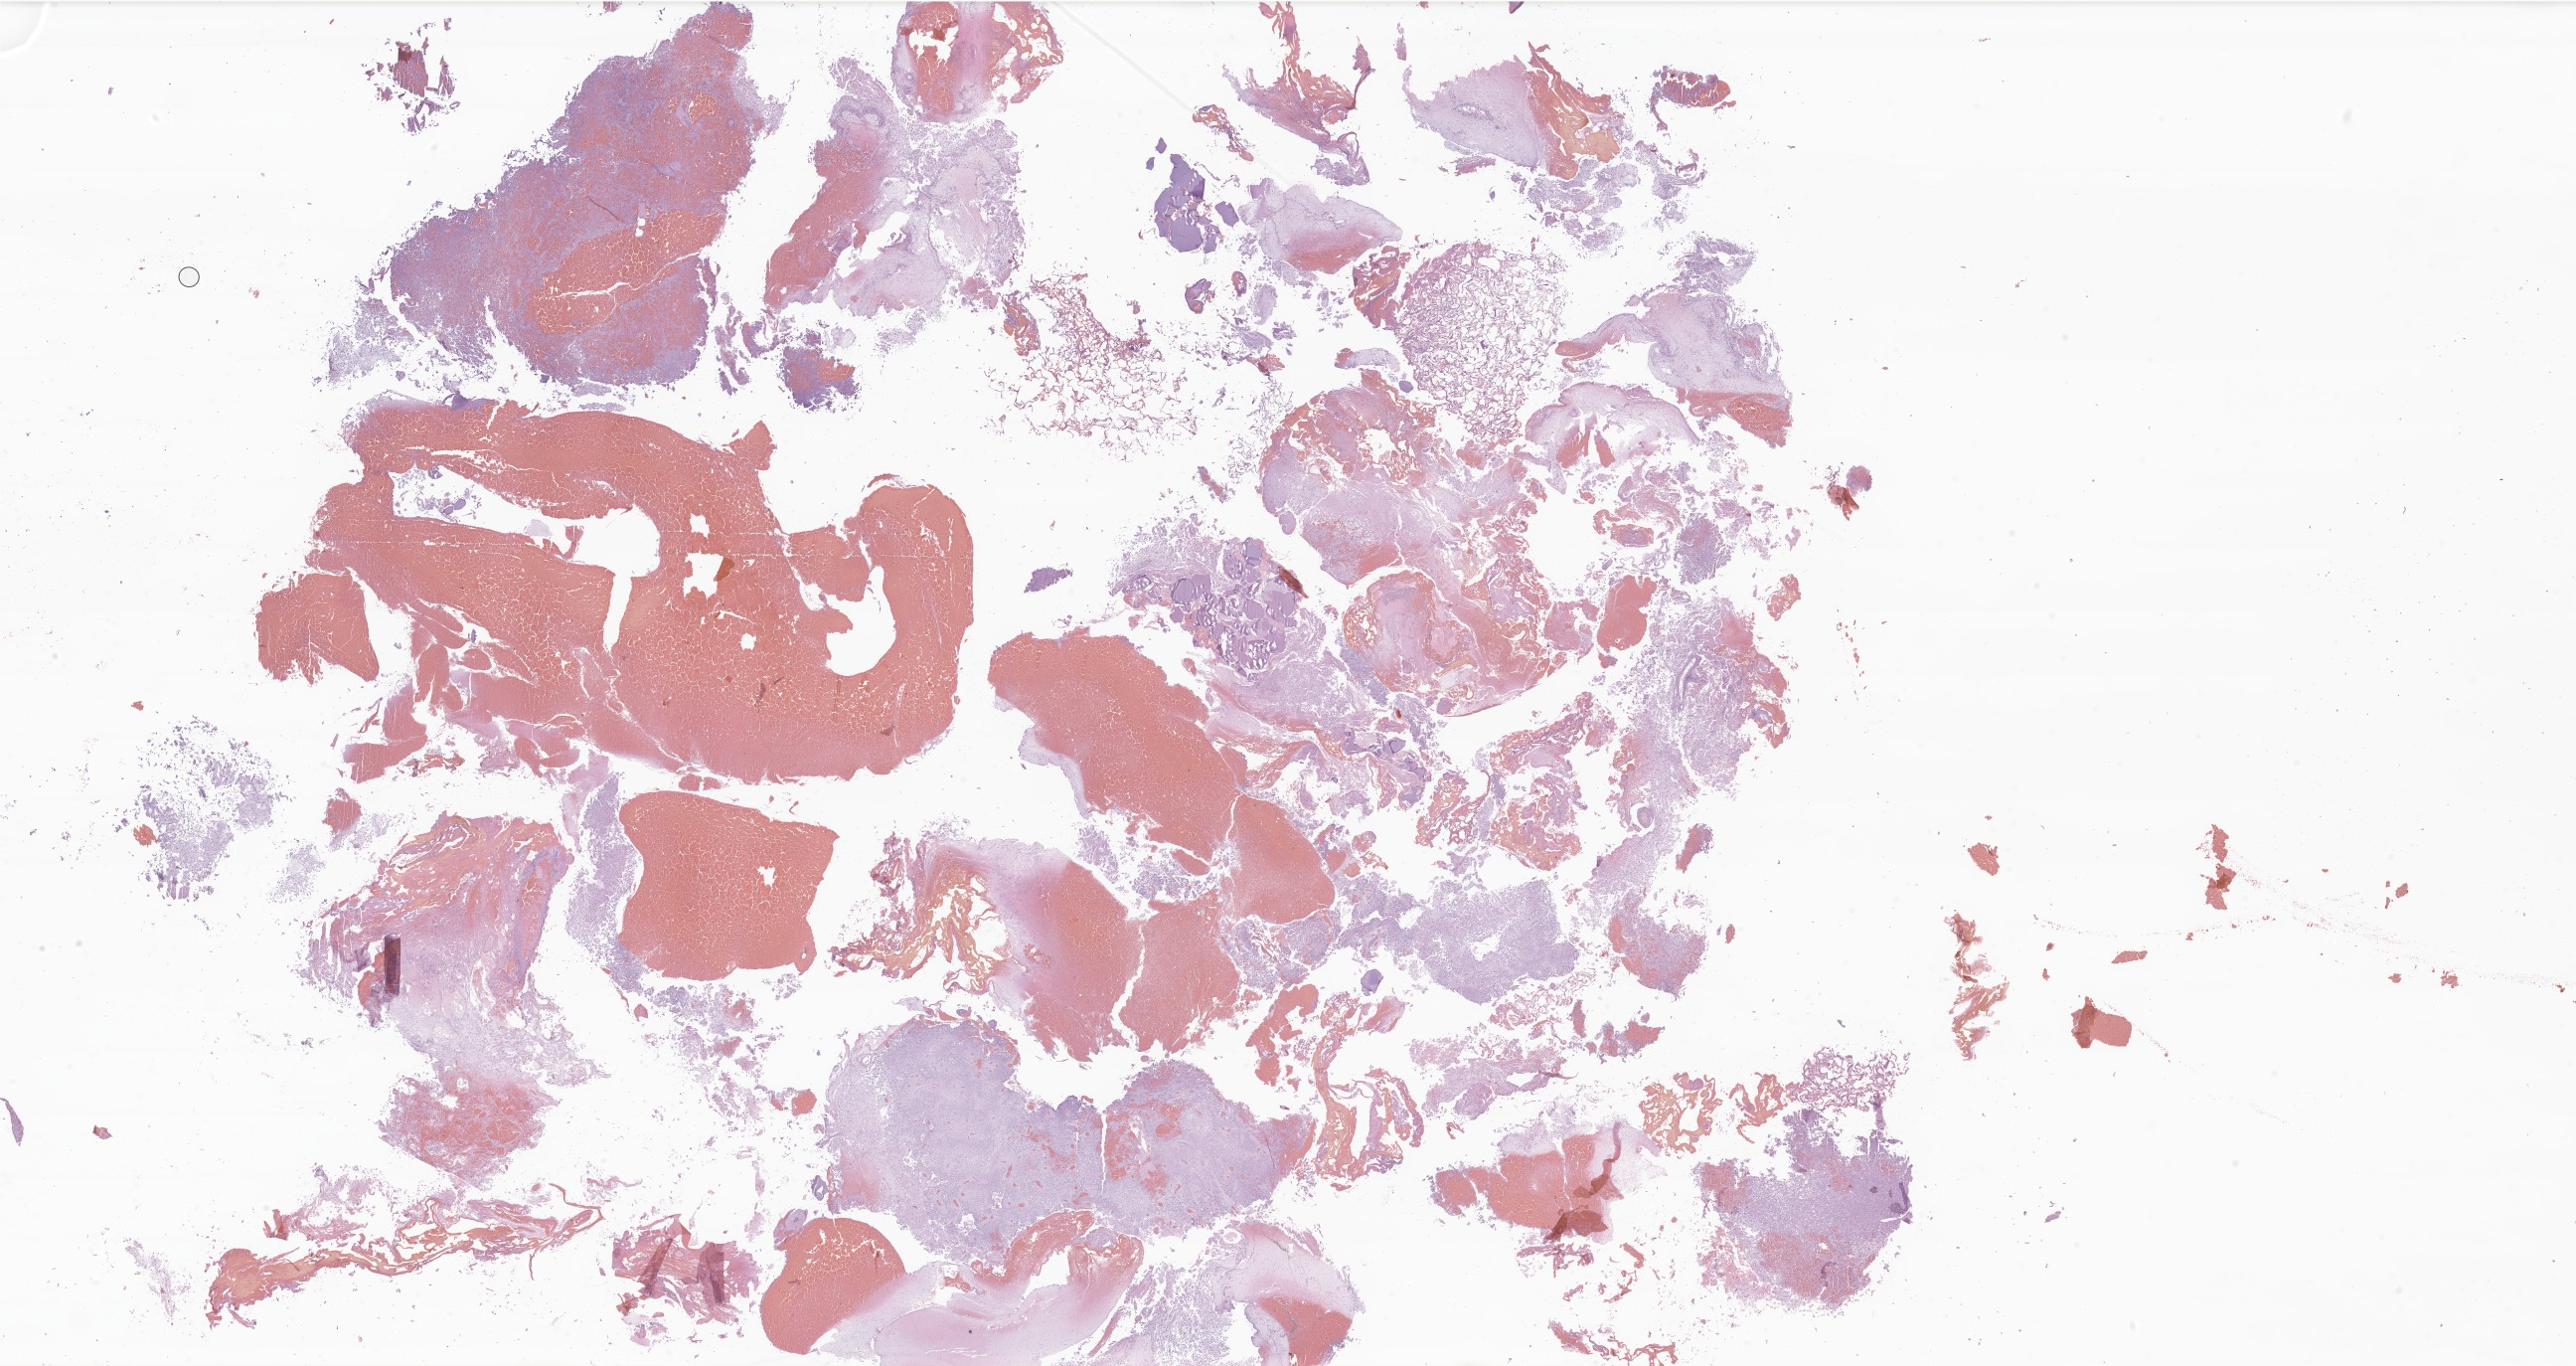
Digitized H&E-stained section of tumor tissue from the brain, shown as a low-resolution overview of the whole scanned area (about 43.7 x 23.2 mm), FFPE section. Female patient, age 64 months (5 years 4 months).
Recorded diagnosis: Ependymoma, NOS.